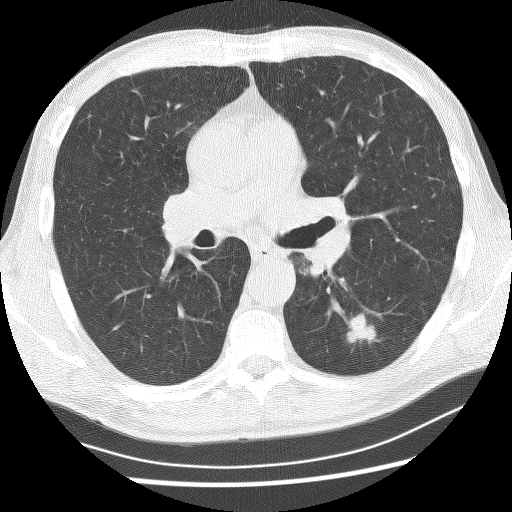
Low-dose screening chest CT, axial slice, first (baseline) screen, lung window (W 1500 / L -600 HU), 120 kVp. Male, age 62 years at enrolment. Current smoker at enrolment.
Lesion marked by an expert reader, box from (x=329, y=306) to (x=384, y=351) px. Screening reader's record for this exam (one nodule recorded; not confirmed to be the boxed lesion): non-calcified nodule or mass ≥4 mm, left lower lobe, 21 × 17 mm, spiculated (stellate) margins, soft tissue attenuation. Official screen result: positive, change unspecified: nodule(s) >= 4 mm or enlarging nodule(s), mass(es), or other non-specific abnormalities suspicious for lung cancer.